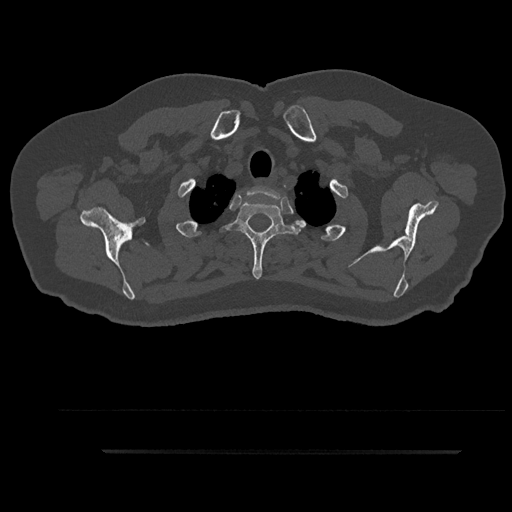
CT including the spine, one axial slice; position 761 of 797 along the scan axis; bone window (W 1800 / L 400 HU); 512 × 512 image matrix, field of view 432 × 432 mm. Male patient, age 63 years. Case-level facts recorded for this patient, not image findings: primary cancer: renal; vertebrae with lytic lesions (as recorded): T8.
Outlined on this slice (semi-automatic segmentation, software-assisted and operator-edited):
- T1 vertebra: box from (x=248, y=186) to (x=284, y=211) px
- T2 vertebra: (x=225, y=201)–(x=303, y=279)